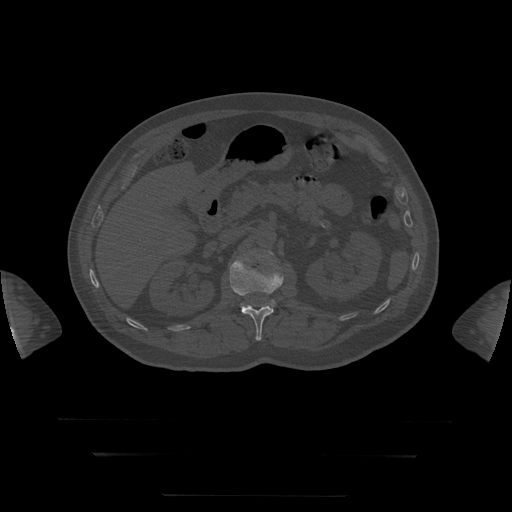
CT including the spine, one axial slice. Slice 42 of 397 in the series (ordered by position). Bone window (W 1800 / L 400 HU). 1.25 mm slice thickness. 512 × 512 image matrix, field of view 510 × 510 mm. Patient age 73 years. From the clinical record (not read from this slice): primary cancer: prostate.
Structures marked on this image (semi-automatic segmentation, software-assisted and operator-edited):
- L1 vertebra: bounding box <230,257,284,341> (left, top, right, bottom; pixels)